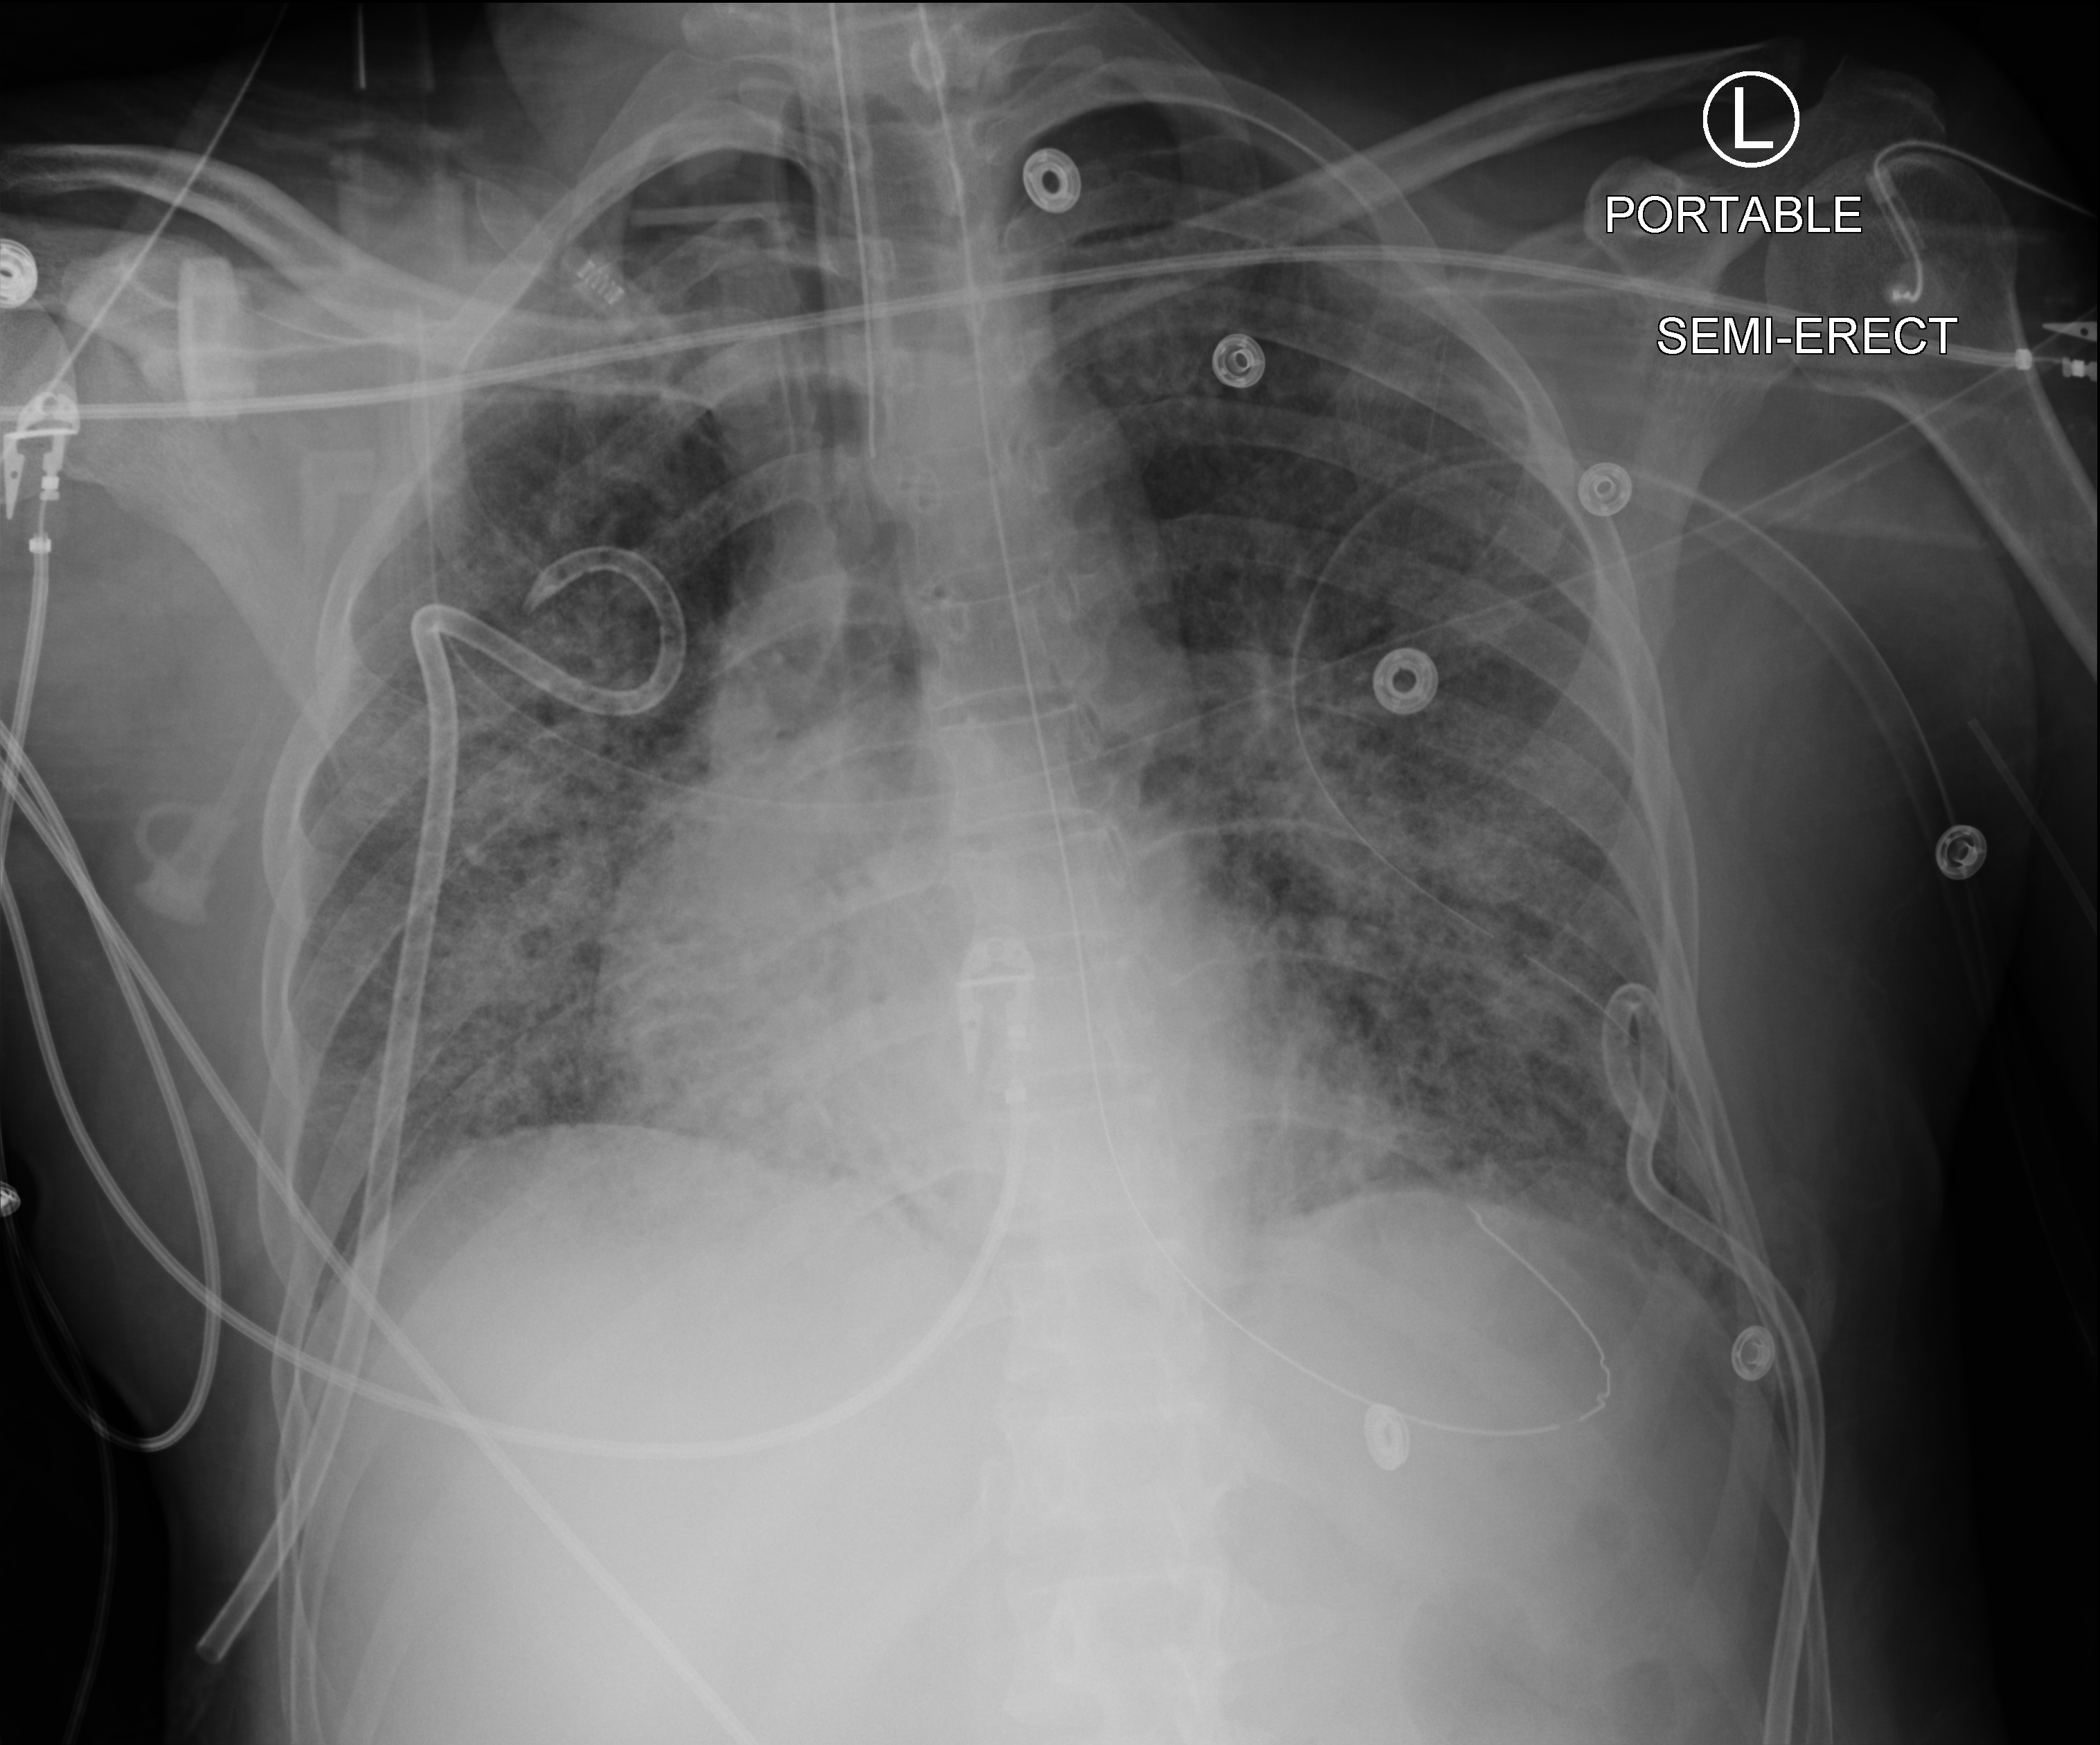
Bedside chest radiograph (computed radiography); anteroposterior (AP) projection. Adult patient hospitalised with COVID-19, age 18–59 years.
From the hospital-stay record, not from the radiograph (when in the stay this image was taken is not recorded):
- other chronic lung disease (admission record): no
- chronic kidney disease (admission record): no
- length of hospital stay: 41 days